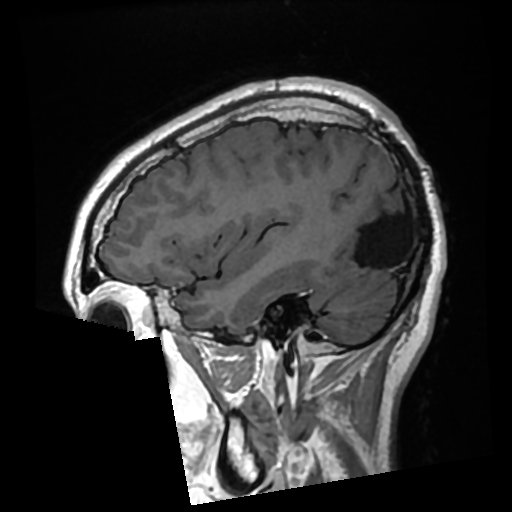
Brain MRI from a brain-tumour surgery series, one sagittal slice. Position 85 of 276 along the scan axis. T1-weighted post-contrast. 0.7 mm slice thickness. 512 × 512 image matrix, field of view 250 × 250 mm. Case-level facts recorded for this patient, not image findings: histopathology: Glioma with ependymal features; WHO grade: 2; tumour location: Left Parietal.
Outlined on this slice (manually delineated by an expert):
- previous resection cavity: bounding box (x1, y1, x2, y2) in pixels: (340, 184, 406, 268)